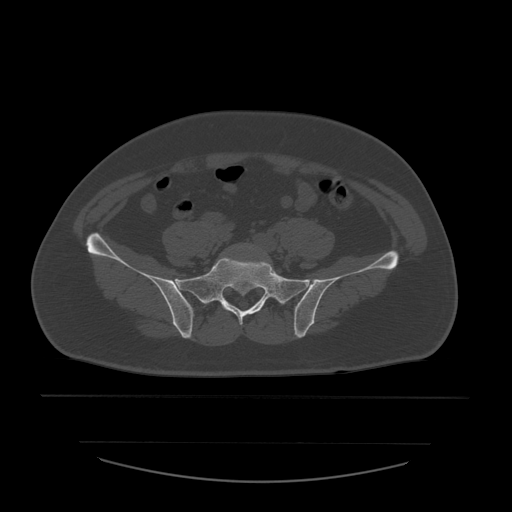
CT including the spine, one axial slice. Position 101 of 532 along the scan axis. Bone window (W 1800 / L 400 HU). 512 × 512 image matrix, field of view 441 × 441 mm. Patient age 44 years. From the clinical record (not read from this slice): primary cancer: soft tissue sarcoma.
Structures marked on this image (semi-automatically segmented with operator editing):
- L5 vertebra: bounding box (x1, y1, x2, y2) in pixels: (239, 244, 257, 251)